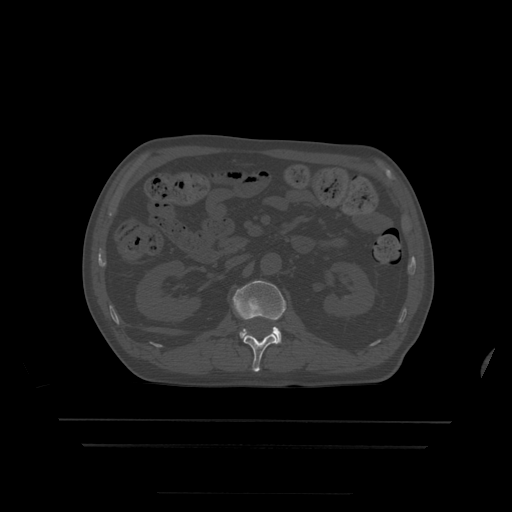
CT including the spine, one axial slice. Position 158 of 522 along the scan axis. Bone window (W 1800 / L 400 HU). 1.25 mm slice thickness. 512 × 512 image matrix, field of view 436 × 436 mm. Patient age 68 years. Case-level facts recorded for this patient, not image findings: primary cancer: urothelial.
Structures marked on this image (semi-automatic segmentation, software-assisted and operator-edited):
- L1 vertebra: box from (x=244, y=333) to (x=277, y=372) px
- L2 vertebra: (x=233, y=281)–(x=287, y=344)